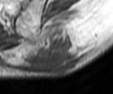
MRI of an extremity soft-tissue mass, one axial slice. Slice 17 of 42 in the series (ordered by position). MR volume resampled by the dataset authors to the PET/CT grid (not the native acquisition matrix). 3.27 mm slice thickness. 113 × 94 image matrix, field of view 110 × 92 mm. Male patient. From the clinical record (not read from this slice): histological type: leiomyosarcoma; grade: intermediate; site of the primary tumour: left pelvis.
Outlined on this slice (expert contour drawn on MRI and transferred to this co-registered scan by the dataset authors):
- gross tumour volume (mass): bounding box <33,34,75,74> (left, top, right, bottom; pixels)